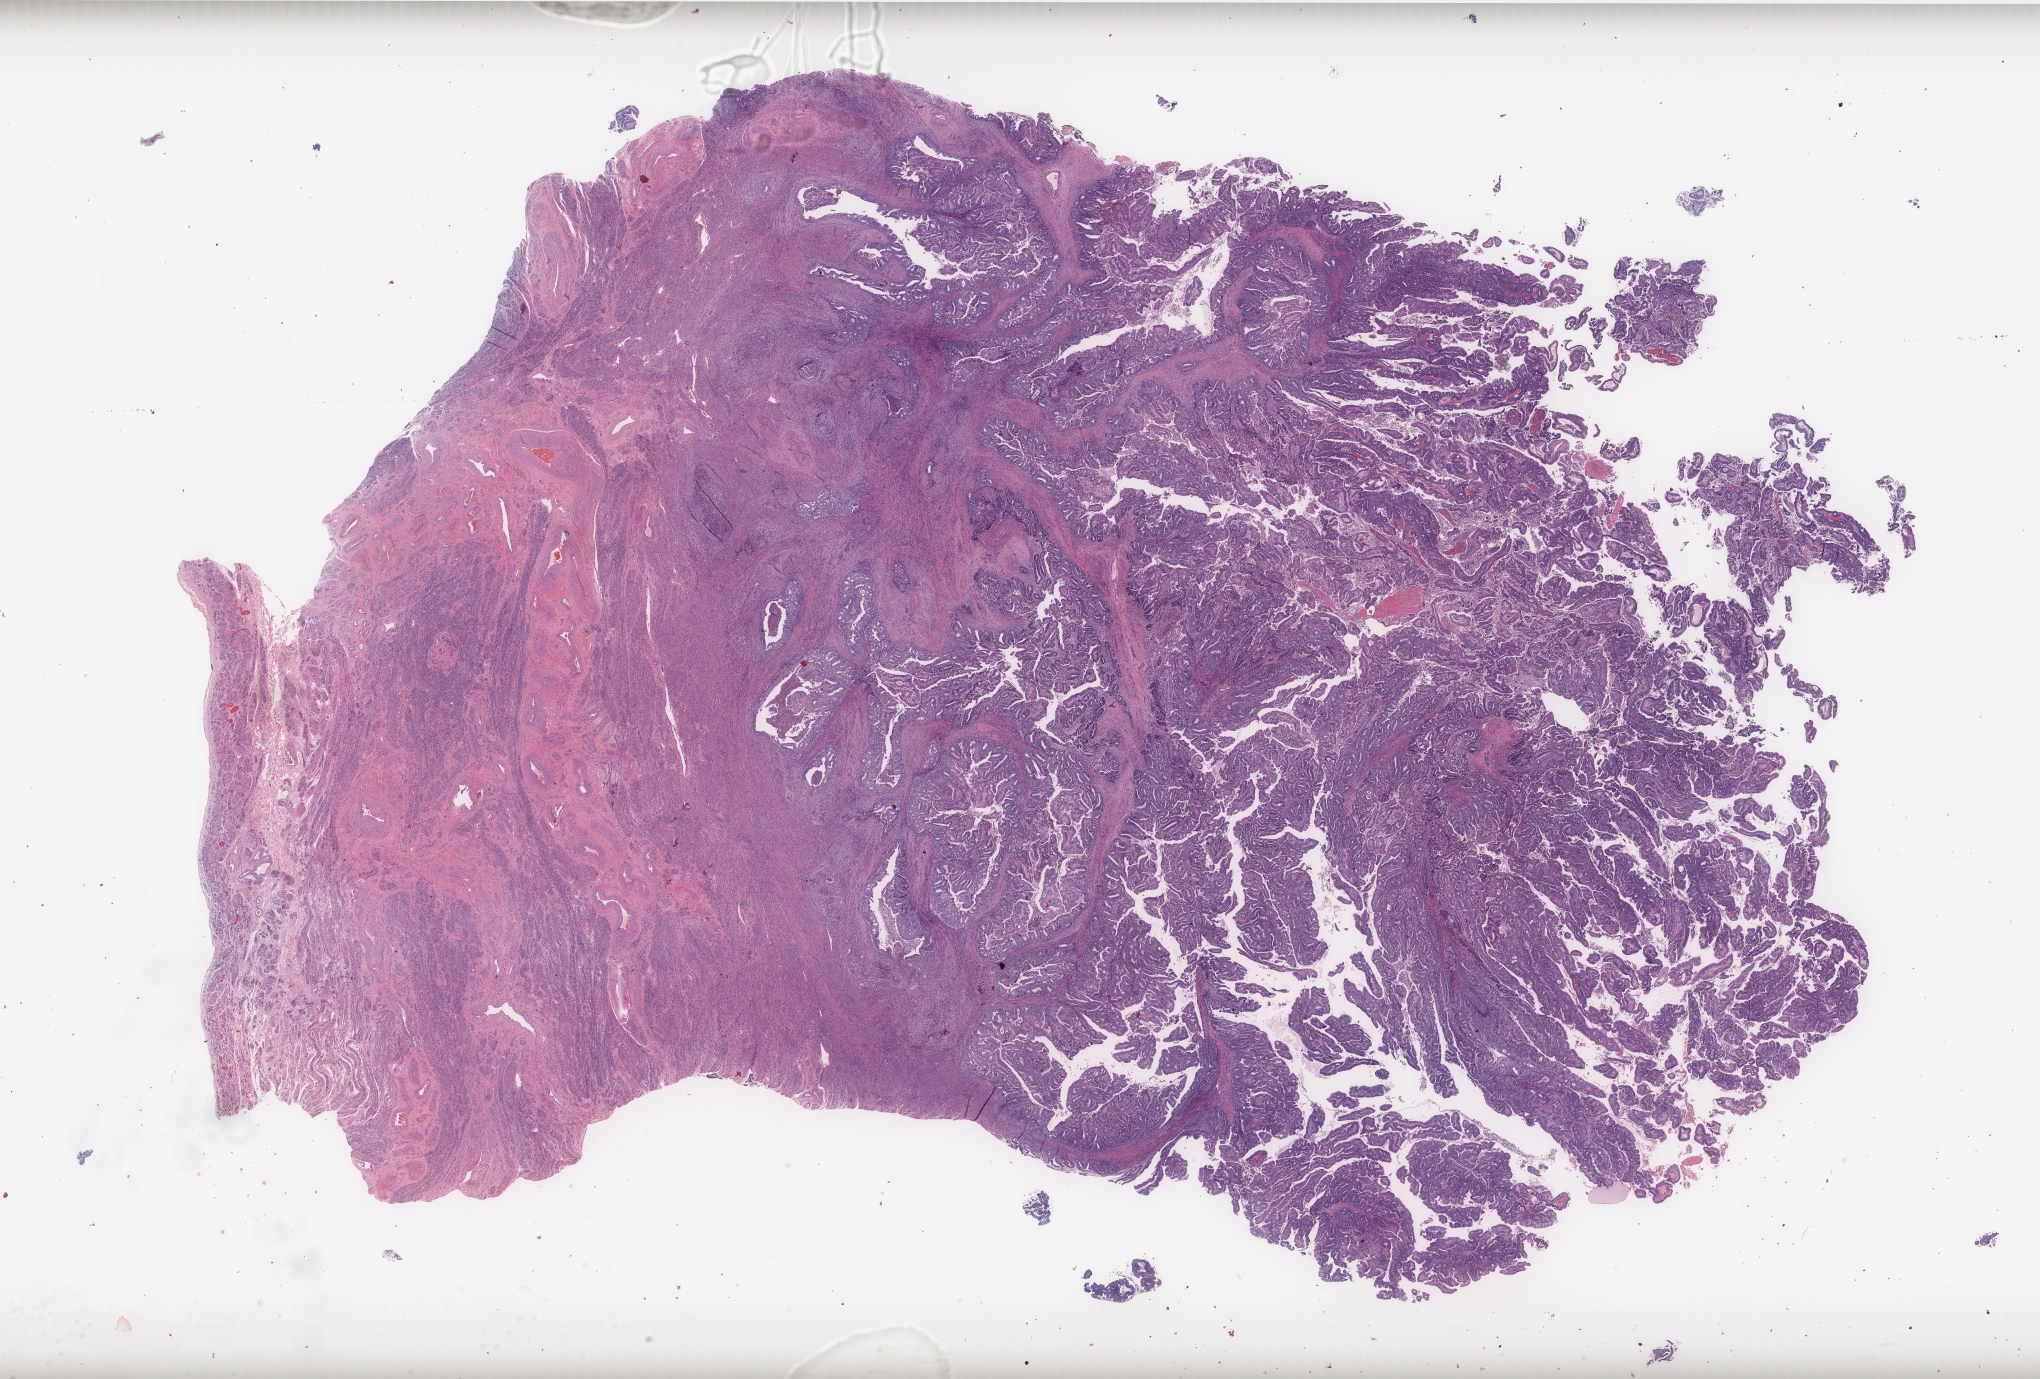
H&E whole-slide image — whole scanned area (about 32.7 x 22.1 mm) shown as a low-resolution overview, formalin-fixed paraffin-embedded (FFPE) diagnostic section, primary tumour sample from the uterus. Female, age 73 years at initial diagnosis. Histologic grade: G2 (moderately differentiated).
- FIGO stage: IB
- pathologic diagnosis: Endometrioid adenocarcinoma, NOS